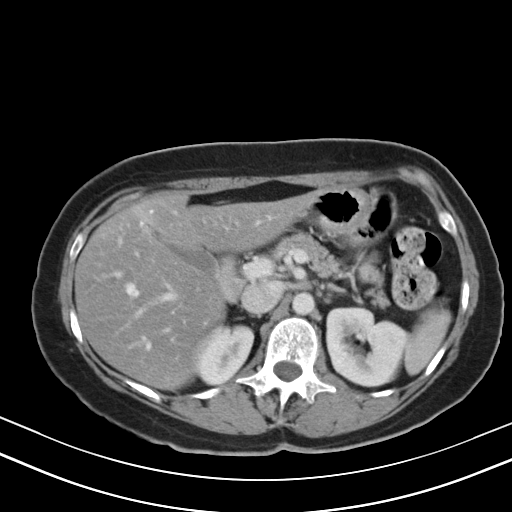
Contrast-enhanced abdominal CT, one axial slice; position 27 of 47 along the scan axis; 130 kVp; soft-tissue window (W 400 / L 40 HU); 5 mm slice thickness; 512 × 512 image matrix, field of view 350 × 350 mm. Female patient. Case-level facts recorded for this patient, not image findings: diagnosis: colorectal cancer liver metastases, imaged before liver resection; multiple liver metastases: no; largest metastasis: 3.5 cm; disease in both lobes: no.
Structures marked on this image (outlined manually by an expert reader):
- hepatic veins: box from (x=116, y=210) to (x=151, y=348) px
- liver: (x=76, y=195)–(x=307, y=389)
- planned liver remnant (the part of the liver to remain after resection): (x=76, y=195)–(x=306, y=389)
- portal vein (with intrahepatic branches): (x=134, y=281)–(x=179, y=318)